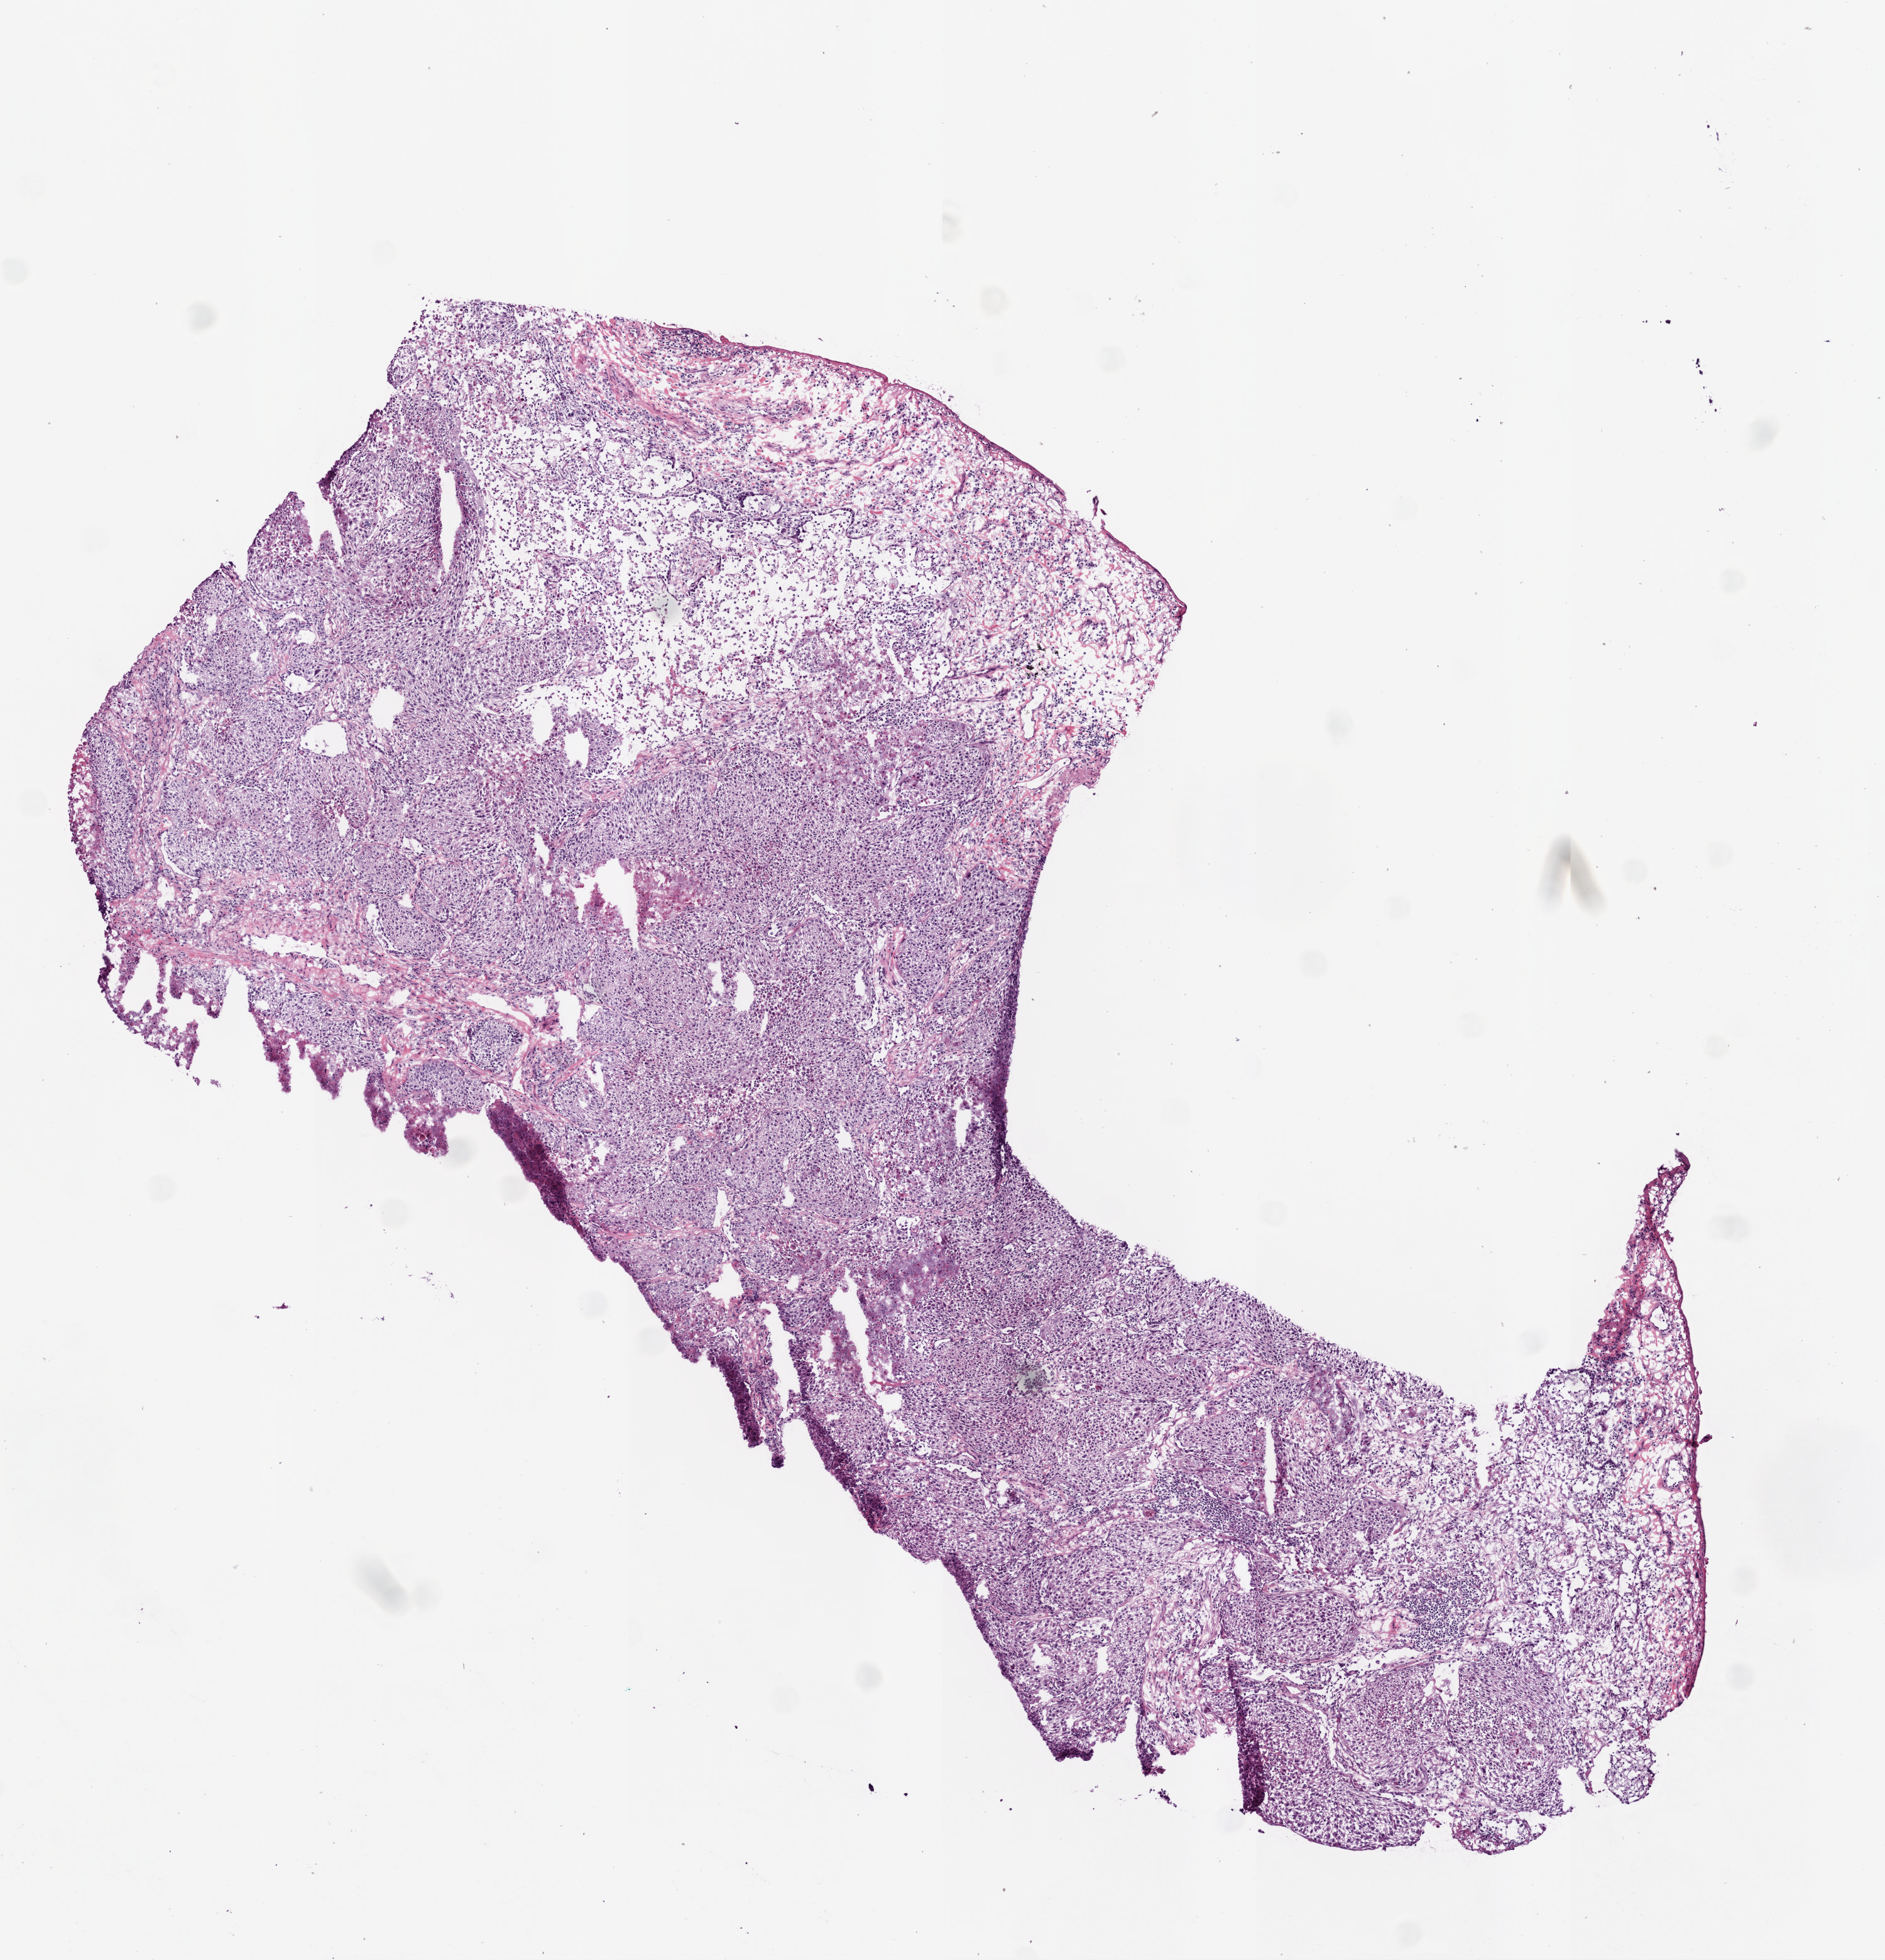
Whole-slide histology image, H&E-stained — a low-resolution overview of the entire scanned area, about 6.0 x 6.3 mm (from a 20x scan). Frozen section from the bottom of the tissue portion. Primary tumour sample from the lung. Patient: female, age at initial diagnosis 68 years. Composition of this section per pathologist review: tumour cells 70%, tumour nuclei 80%, normal cells 20%, stromal cells 5%, necrosis 5%.
• AJCC pathologic stage: IIIB
• pathologic diagnosis: Squamous cell carcinoma, NOS (lower lobe, lung)